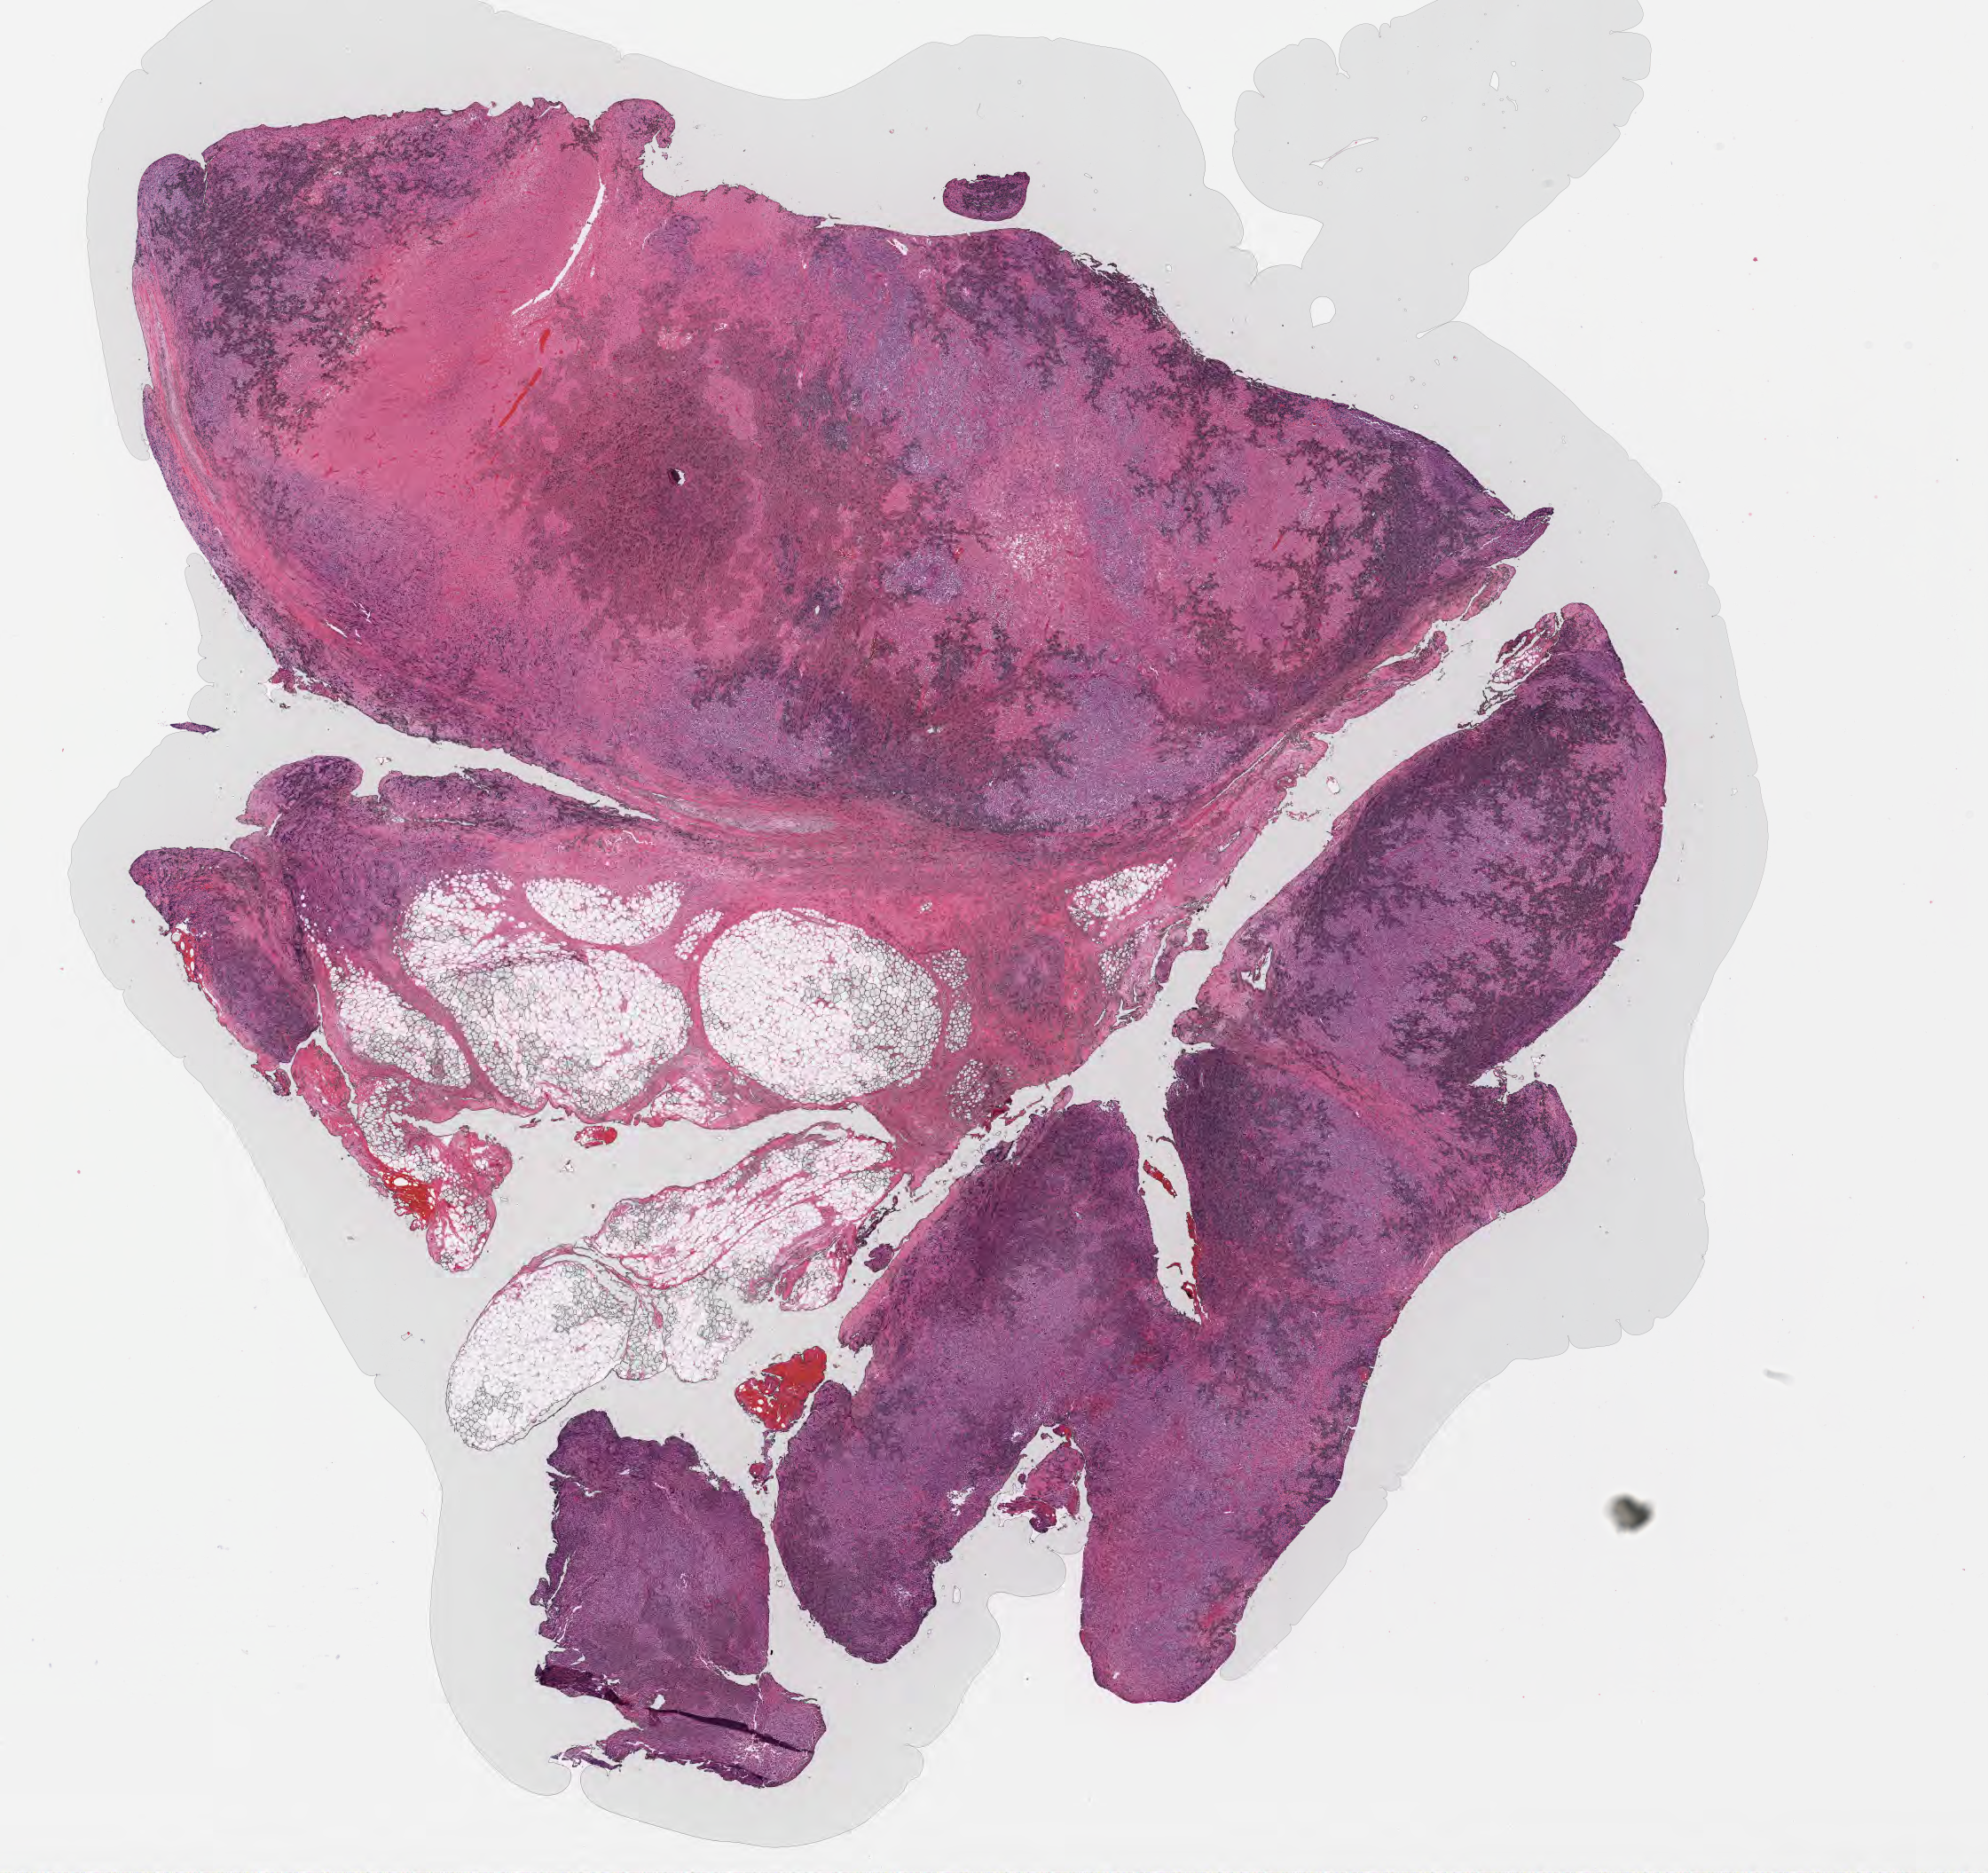
Whole-slide image, H&E stain — low-resolution overview of the scanned area, about 18.1 x 17.1 mm; specimen: tumor tissue. Patient: female, age 46 years.
Diagnosis: Diffuse large B-cell lymphoma, NOS.